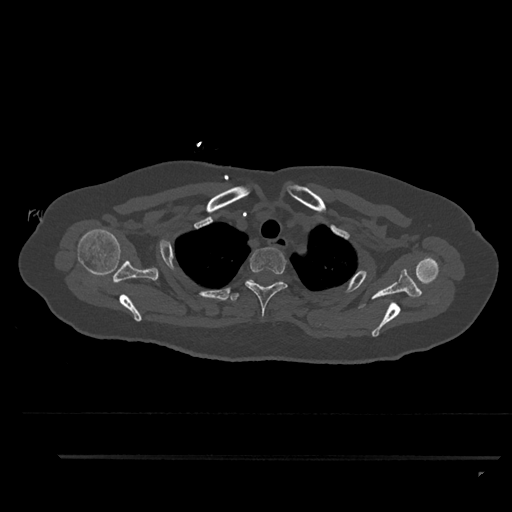
CT including the spine, one axial slice; slice 717 of 797 in the series (ordered by position); reconstruction kernel Br40s/3; 120 kVp; bone window (W 1800 / L 400 HU); 0.5 mm slice thickness; 512 × 512 image matrix. Patient: female, 44 years. From the clinical record (not read from this slice): primary cancer: renal; vertebrae with lytic lesions (as recorded): L1.
Outlined on this slice (semi-automatic segmentation, software-assisted and operator-edited):
- T2 vertebra: box from (x=245, y=247) to (x=288, y=317) px
- T3 vertebra: (x=228, y=280)–(x=254, y=301)